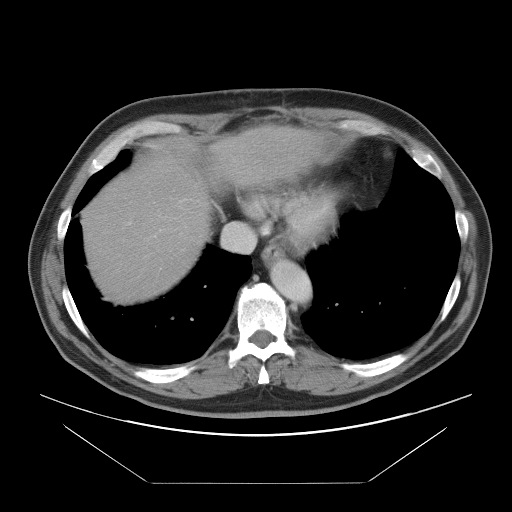
Contrast-enhanced abdominal CT, one axial slice. Position 83 of 97 along the scan axis. 120 kVp. Intravenous contrast given. Soft-tissue window (W 400 / L 40 HU). 5 mm slice thickness. 512 × 512 image matrix, field of view 442 × 442 mm. Male patient, age 62 years. Case-level facts recorded for this patient, not image findings: diagnosis: colorectal cancer liver metastases, imaged before liver resection; multiple liver metastases: no; largest metastasis: 7 cm; disease in both lobes: yes.
Annotated regions visible in this slice (outlined manually by an expert reader):
- hepatic veins: bounding box <222,223,255,253> (left, top, right, bottom; pixels)
- liver: <84,131,309,301>
- planned liver remnant (the part of the liver to remain after resection): <84,179,209,300>
- portal vein (with intrahepatic branches): <160,200,184,231>